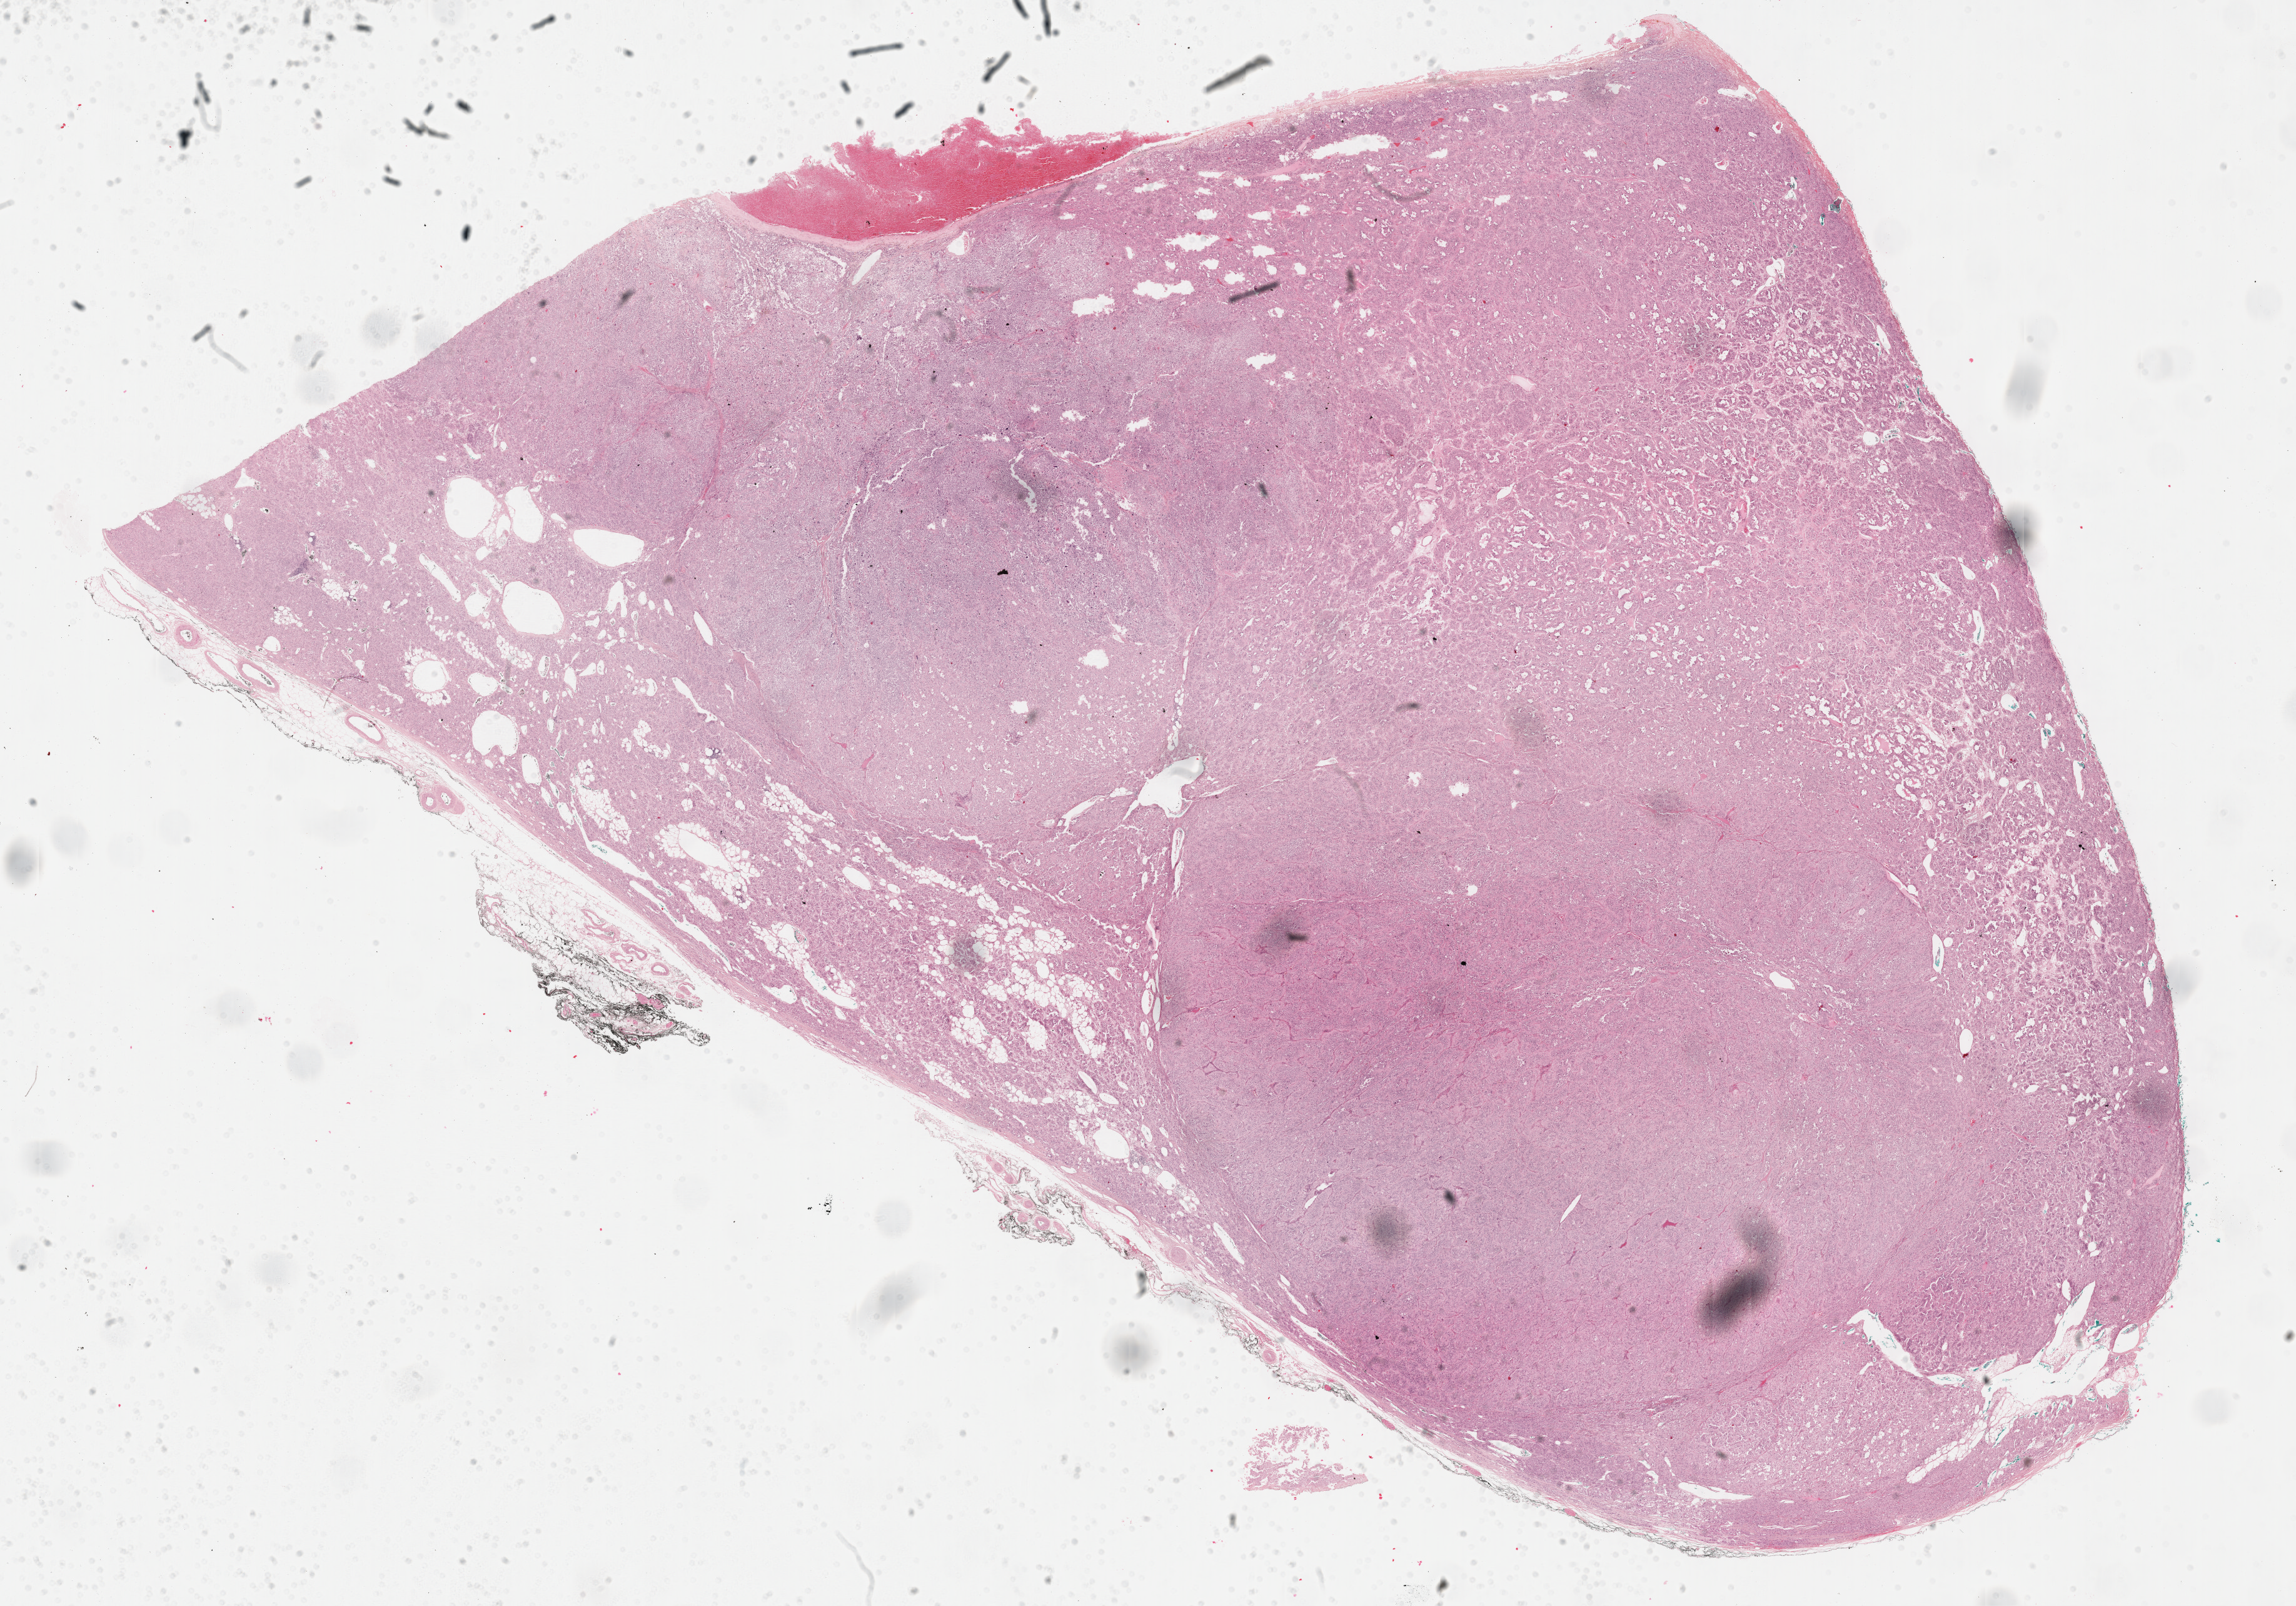
Hematoxylin and eosin (H&E) stained whole-slide image — shown as a low-resolution overview of the whole scanned area (about 29.7 x 20.8 mm, acquisition: 40x scan); formalin-fixed paraffin-embedded (FFPE) diagnostic section; primary tumour sample from the adrenal cortex. Patient: female, age at initial diagnosis 69 years.
Laterality: left. Pathologic diagnosis: Adrenal cortical carcinoma (cortex of adrenal gland).